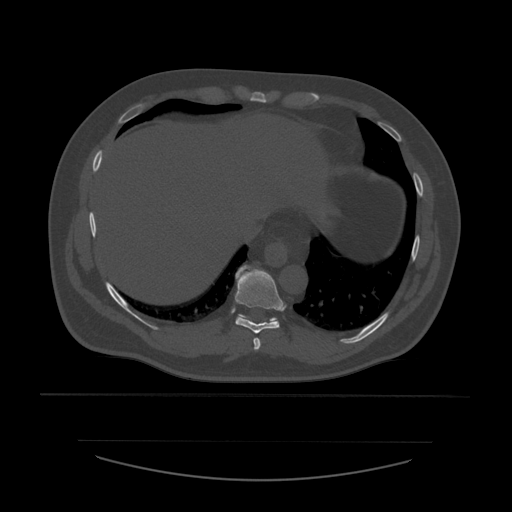
CT including the spine, one axial slice; position 314 of 532 along the scan axis; bone window (W 1800 / L 400 HU); 1.25 mm slice thickness; 512 × 512 image matrix, field of view 441 × 441 mm. Patient age 44 years. Case-level facts recorded for this patient, not image findings: primary cancer: soft tissue sarcoma.
Structures marked on this image (semi-automatically segmented with operator editing):
- T10 vertebra: bounding box (x1, y1, x2, y2) in pixels: (239, 315, 277, 321)
- T8 vertebra: (253, 338, 261, 350)
- T9 vertebra: (235, 266, 284, 334)